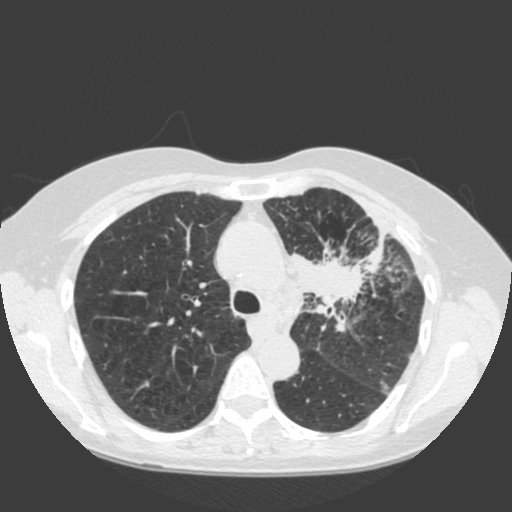
Axial slice from a low-dose chest CT screening exam, baseline annual screen, lung window (W 1500 / L -600 HU), standard (soft-tissue) reconstruction kernel (C), 512 × 512 image matrix, field of view 350 × 350 mm. Female, age 66 years at enrolment. Current smoker at enrolment.
Expert reader's lesion annotation, bounding box [x1, y1, x2, y2] px = [284, 234, 398, 336]. The exam's reader record, not a measurement of the box and not confirmed to be the same lesion: non-calcified nodule or mass ≥4 mm, left upper lobe, 61 × 45 mm, spiculated (stellate) margins, soft tissue attenuation. Lung cancer was diagnosed 19 days after this screen: squamous cell carcinoma, keratinizing, NOS, left upper lobe, left hilum, mediastinum, left main stem bronchus, other location, poorly differentiated (G3), stage IIIB (AJCC 6th edition), 60 mm at pathology.